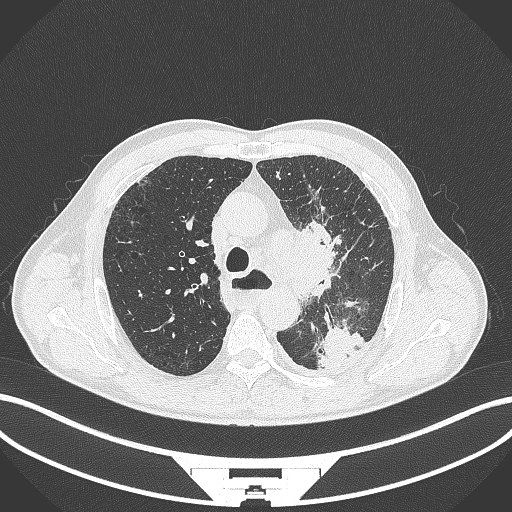
Chest CT, one axial slice. Position 272 of 411 along the scan axis. 120 kVp. Lung window (W 1500 / L -600 HU). 1 mm slice thickness. 512 × 512 image matrix, field of view 400 × 400 mm. Patient: male, 57 years. Case-level facts recorded for this patient, not image findings: clinical TNM (as recorded): T2a N1 M0.
Outlined on this slice (rectangle marked by the reading radiologist):
- lung tumour (recorded histology: squamous cell carcinoma): bounding box <287,226,341,306> (left, top, right, bottom; pixels)